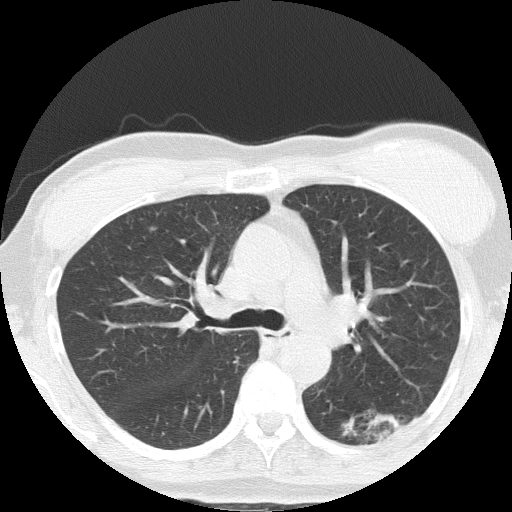
Low-dose screening chest CT, axial slice; third screening round (two years after baseline); lung window (W 1500 / L -600 HU); 2 mm slice thickness; 120 kVp; 512 × 512 image matrix, field of view 308 × 308 mm. Female, age 64 years at enrolment. Former smoker at enrolment.
Expert-annotated lung lesion, bounding box <344,389,430,457> (left, top, right, bottom; pixels). The screening reader recorded 3 non-calcified nodules or masses ≥4 mm on this exam; which of them this box marks is not recorded. Official screen result: positive, other.